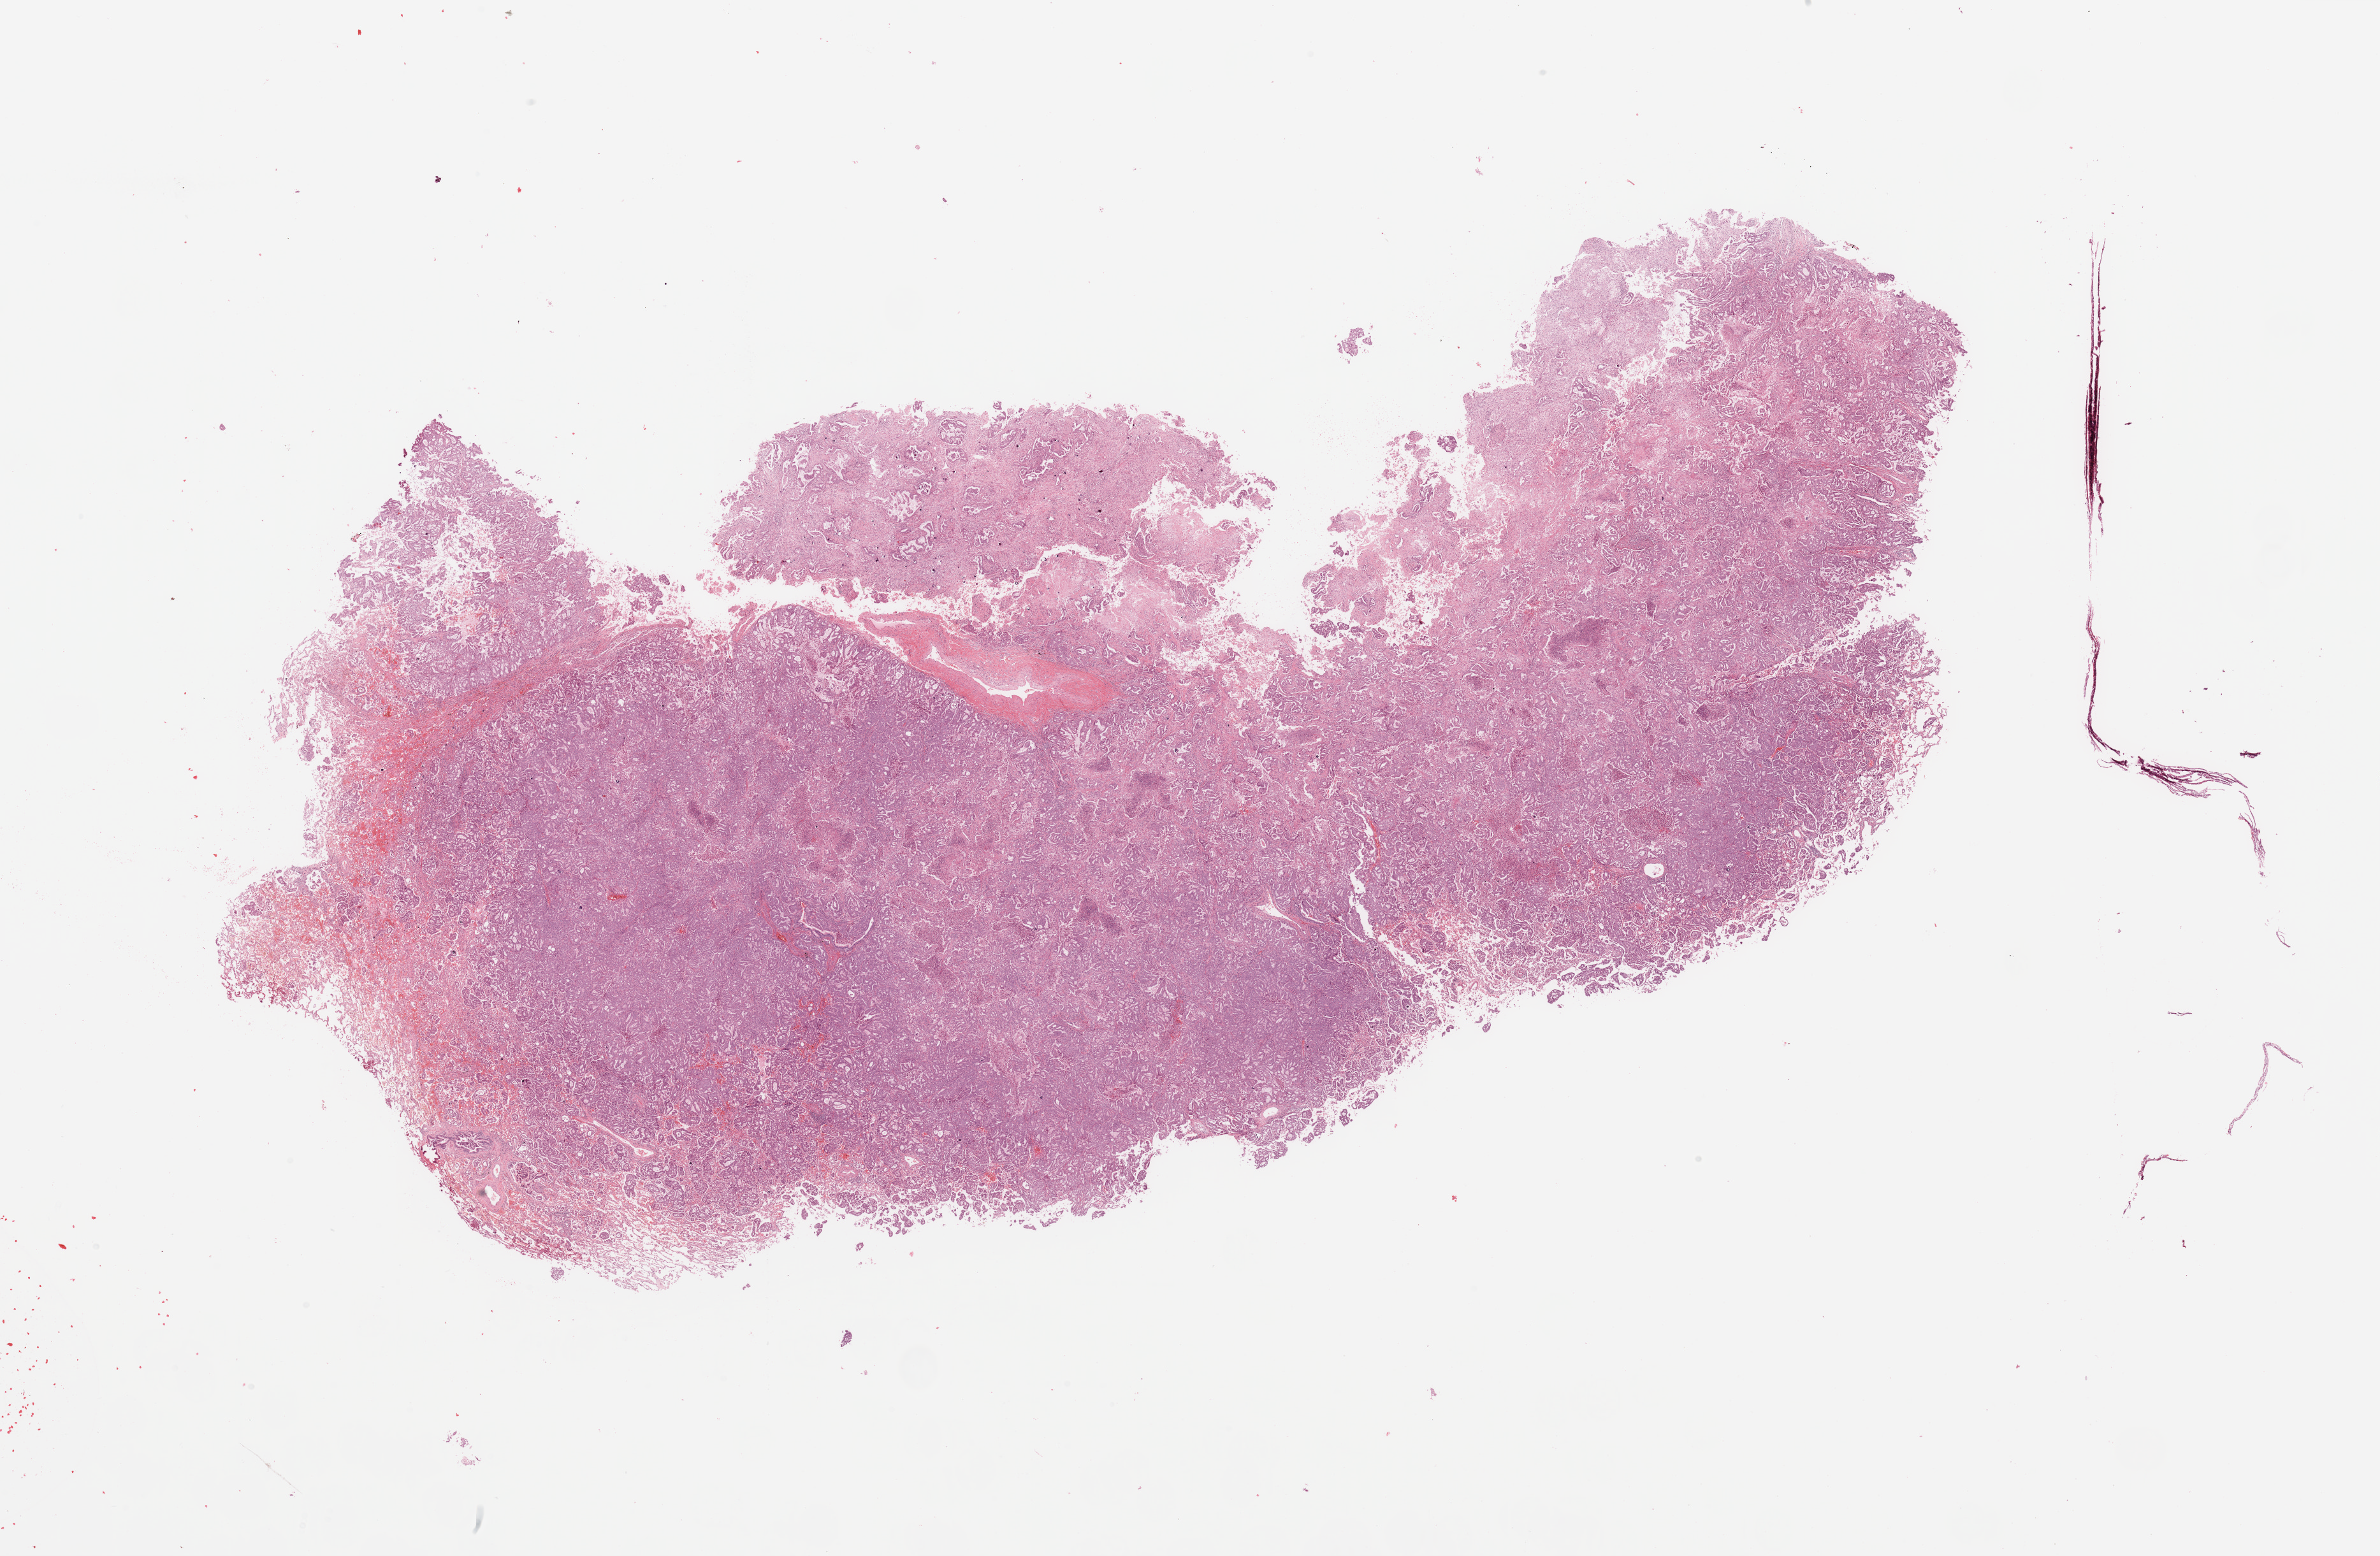
Whole-slide histology image, H&E-stained — whole scanned area (about 29.5 x 19.3 mm, from a 20x scan) shown as a low-resolution overview. Tumour tissue sample, lung. Patient: male, age 58 years. Histologic grade: G2 (moderately differentiated).
Primary tumour site (as recorded): left lower lobe. Diagnosis: Adenocarcinoma, NOS. AJCC pathologic stage: IB.